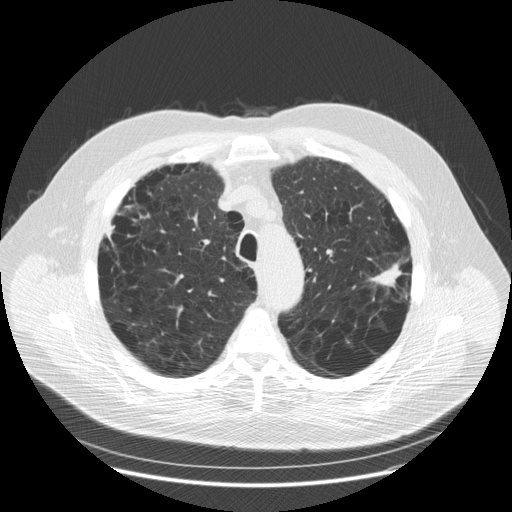
Low-dose screening chest CT, one axial slice. Position 136 of 179 along the scan axis. Reconstruction kernel STANDARD. 120 kVp. Lung window (W 1500 / L -600 HU). 512 × 512 image matrix, field of view 404 × 404 mm.
Structures marked on this image (outlined manually by an expert reader):
- lesion 1 (tumor, upper lobe of left lung): bounding box [x1, y1, x2, y2] px = [369, 261, 403, 288]